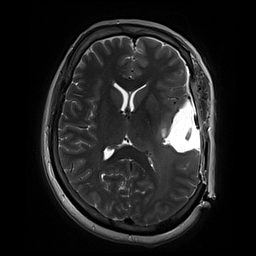
Brain MRI from a brain-tumour surgery series, one axial slice; position 36 of 70 along the scan axis; 256 × 256 image matrix, field of view 220 × 220 mm. Case-level facts recorded for this patient, not image findings: histopathology: Glioblastoma; WHO grade: 4.
Structures marked on this image (outlined manually by an expert reader):
- residual tumour: box from (x=154, y=113) to (x=173, y=142) px